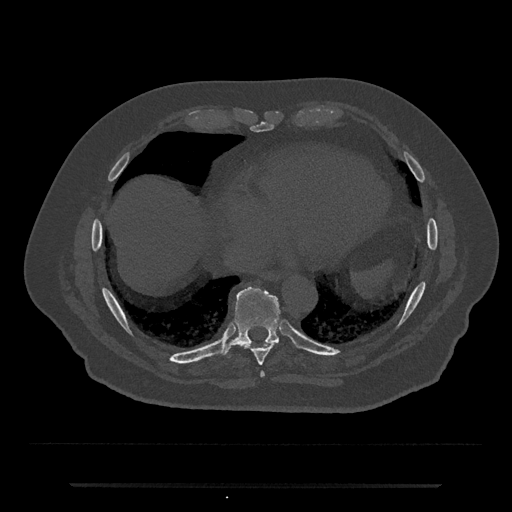
CT including the spine, one axial slice; reconstruction kernel Br40s/3; 120 kVp; bone window (W 1800 / L 400 HU); 0.5 mm slice thickness; 512 × 512 image matrix, field of view 434 × 434 mm. Patient: male, 80 years. Case-level facts recorded for this patient, not image findings: primary cancer: prostate.
Annotated regions visible in this slice (semi-automatically segmented with operator editing):
- T8 vertebra: bounding box (x1, y1, x2, y2) in pixels: (246, 343, 277, 366)
- T9 vertebra: (218, 287, 281, 358)